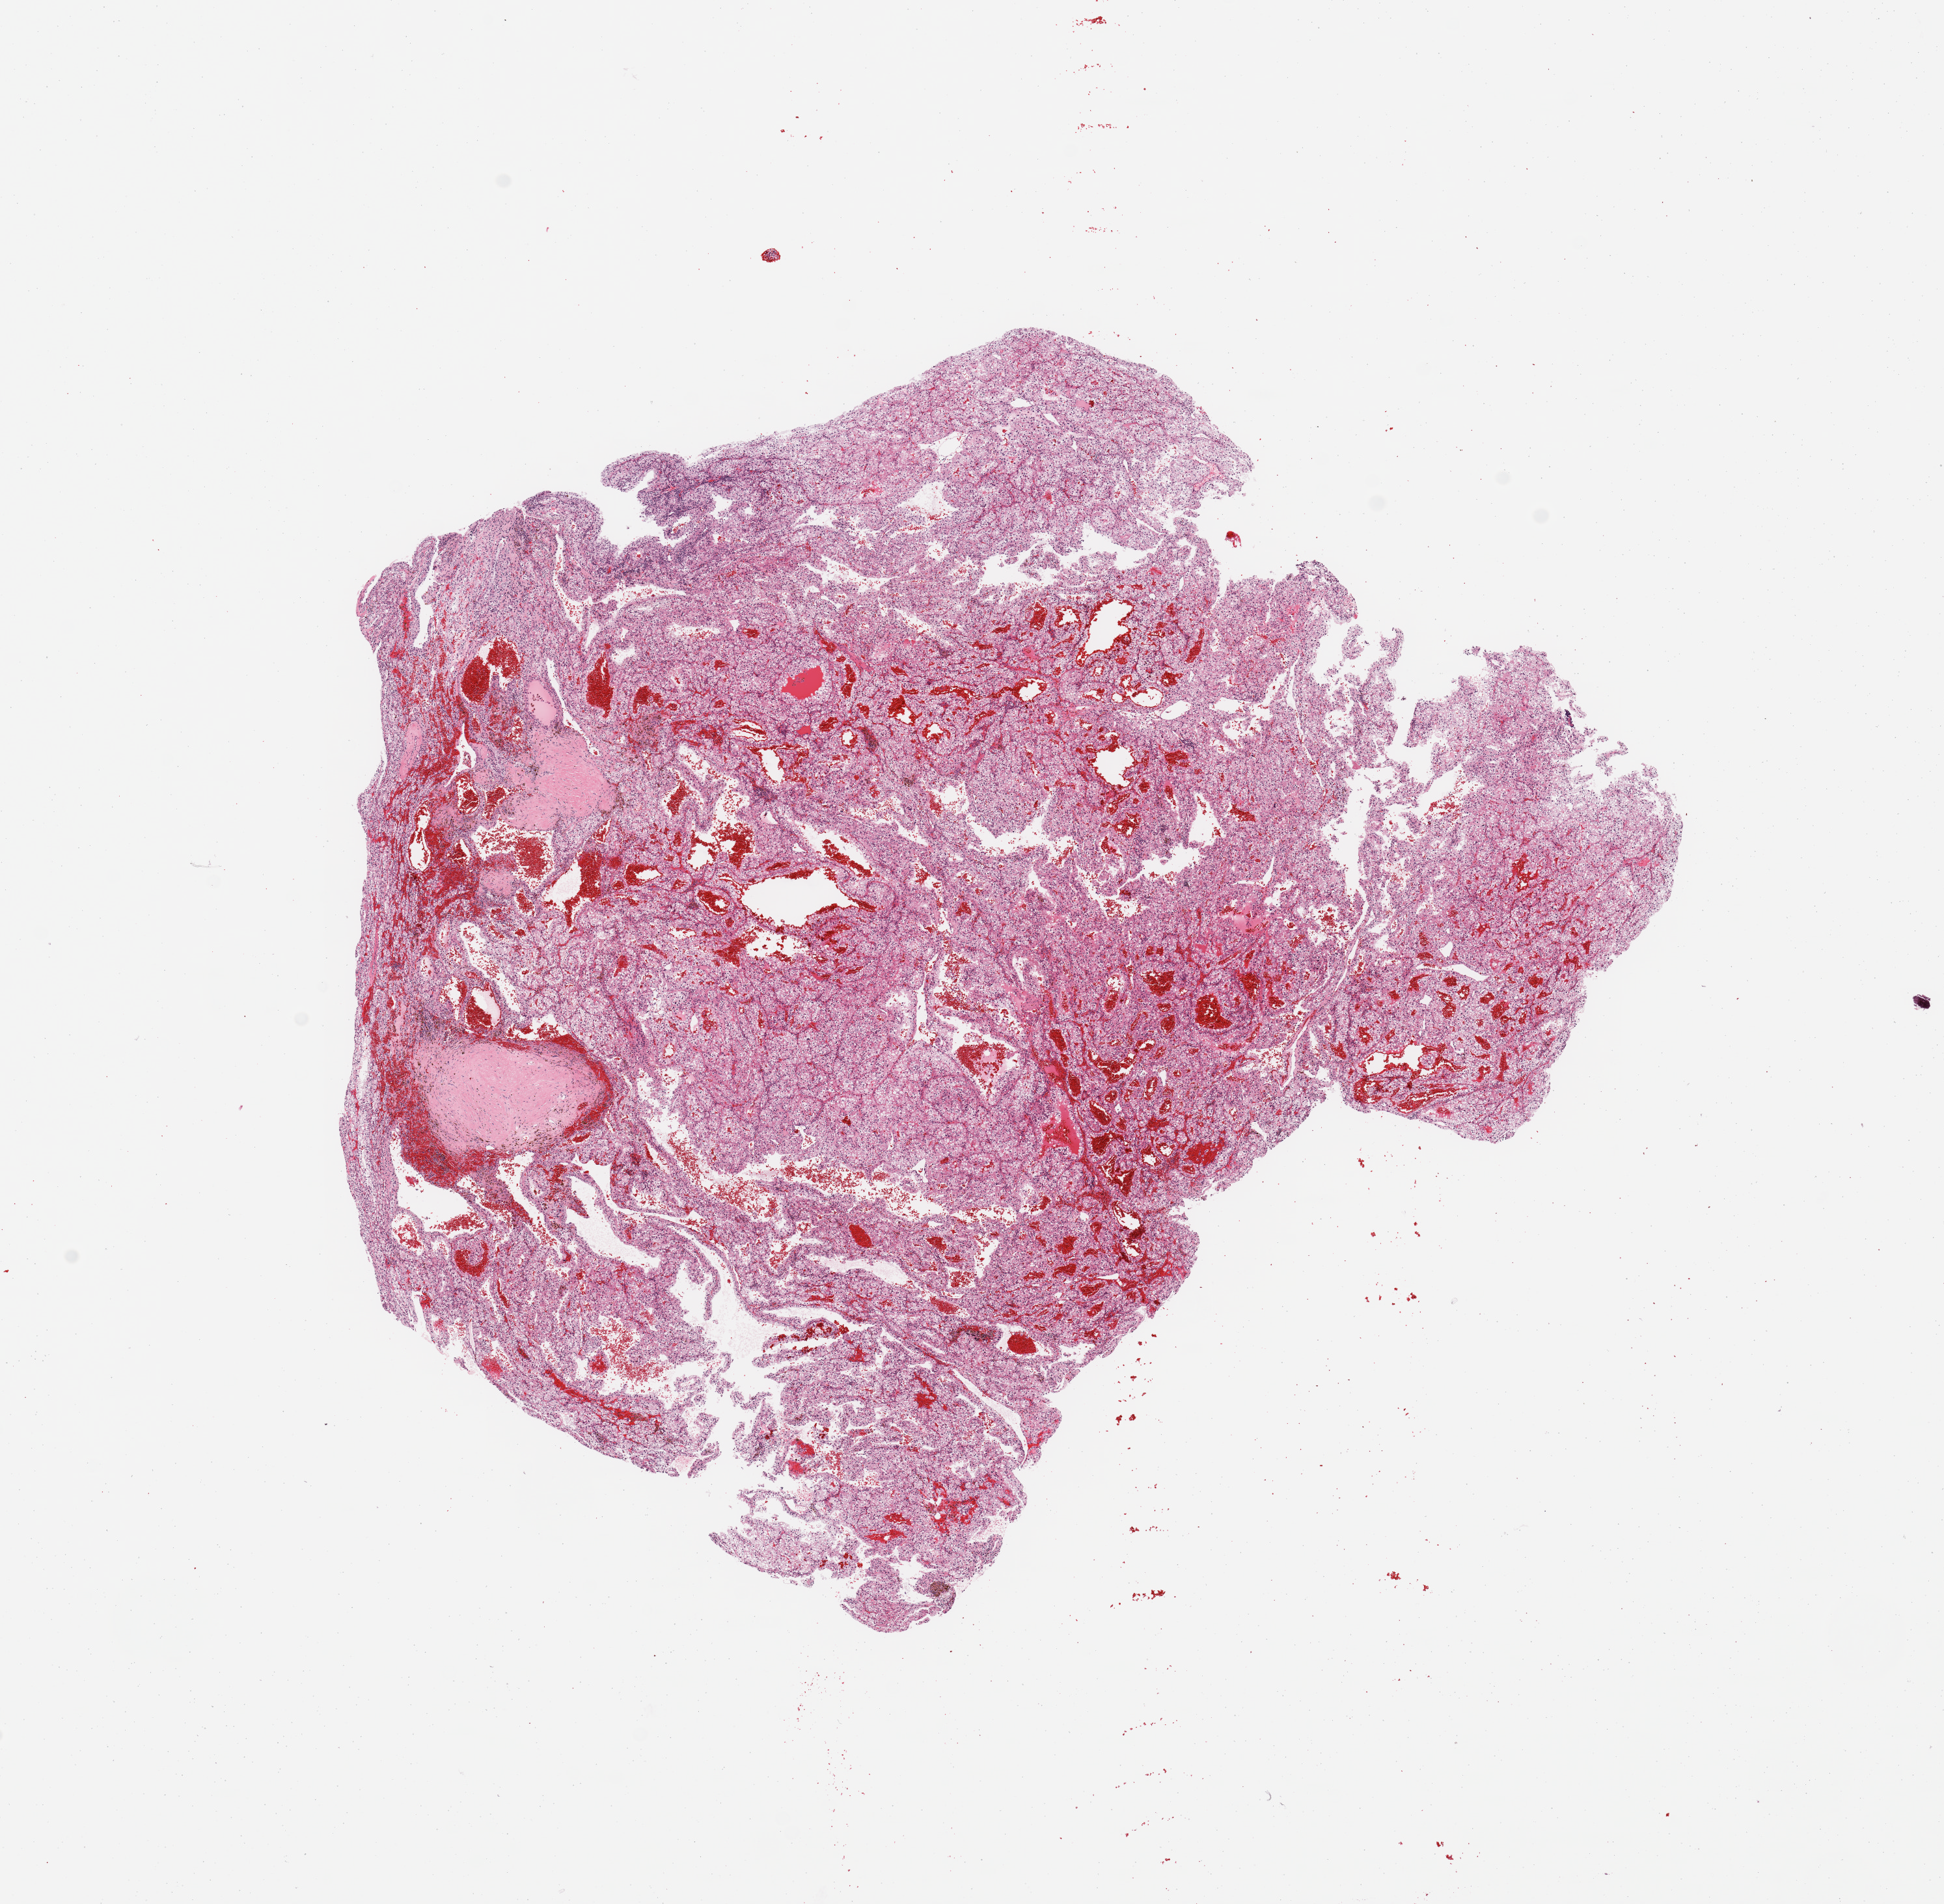
H&E whole-slide image, whole scanned area (about 11.8 x 11.6 mm) shown as a low-resolution overview; tumour tissue sample, sampled site: kidney. 65-year-old female patient. Histologic grade: G3 (poorly differentiated). Composition of this section per pathologist review: tumour nuclei 95%, necrosis 0%.
- histologic diagnosis: Renal cell carcinoma, NOS
- AJCC pathologic stage: I